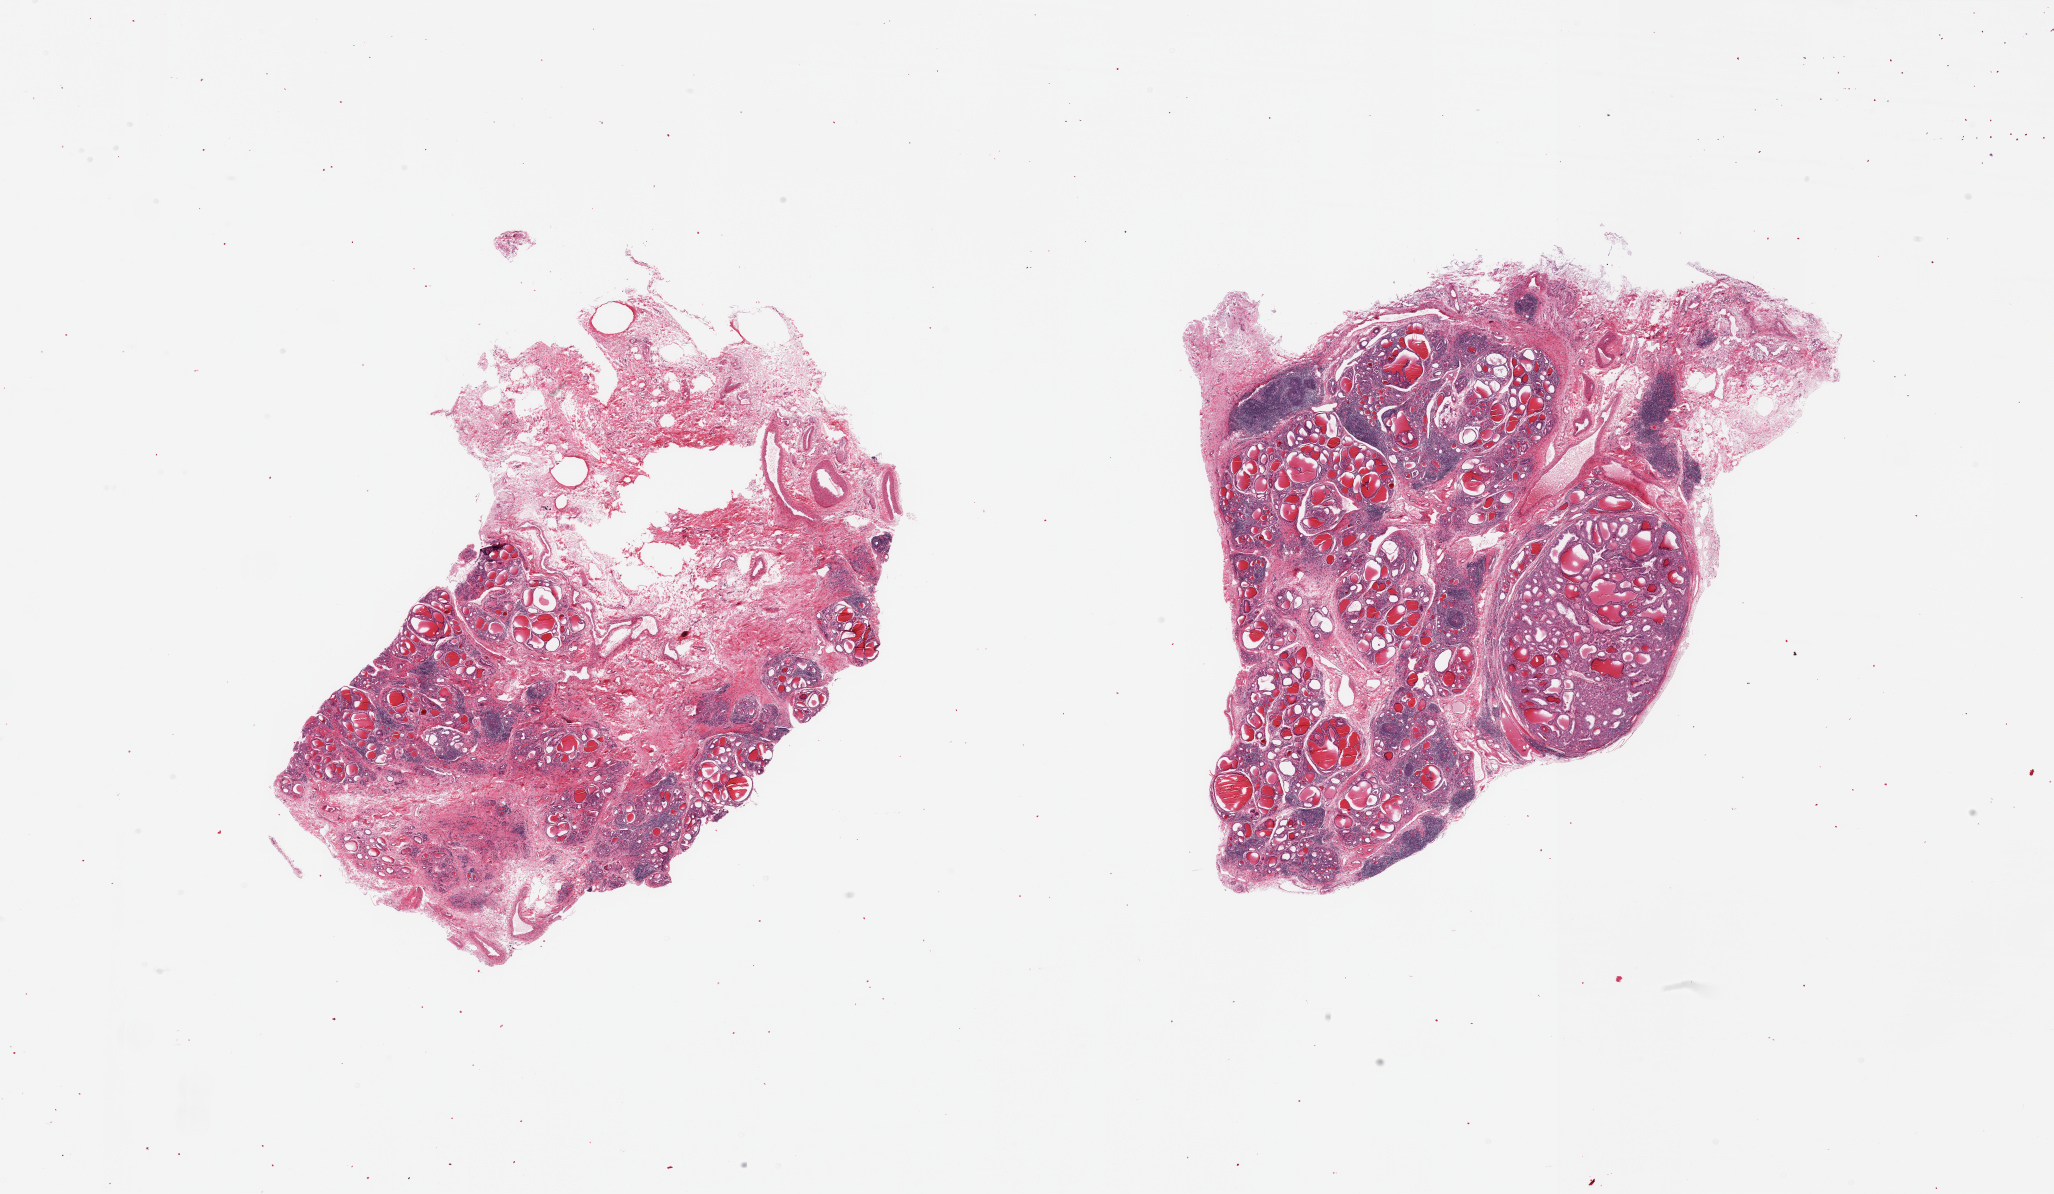
Digitized haematoxylin and eosin-stained section, brightfield — low-resolution overview of the scanned area, about 32.5 x 18.9 mm (acquisition: 20x scan), PAXgene-fixed, paraffin-embedded tissue, section of thyroid (target tissue), donor tissue sample.
Pathologist's review note for this sample: 2 pieces; Hashimoto's thyroiditis in a background of multinodular goiter.